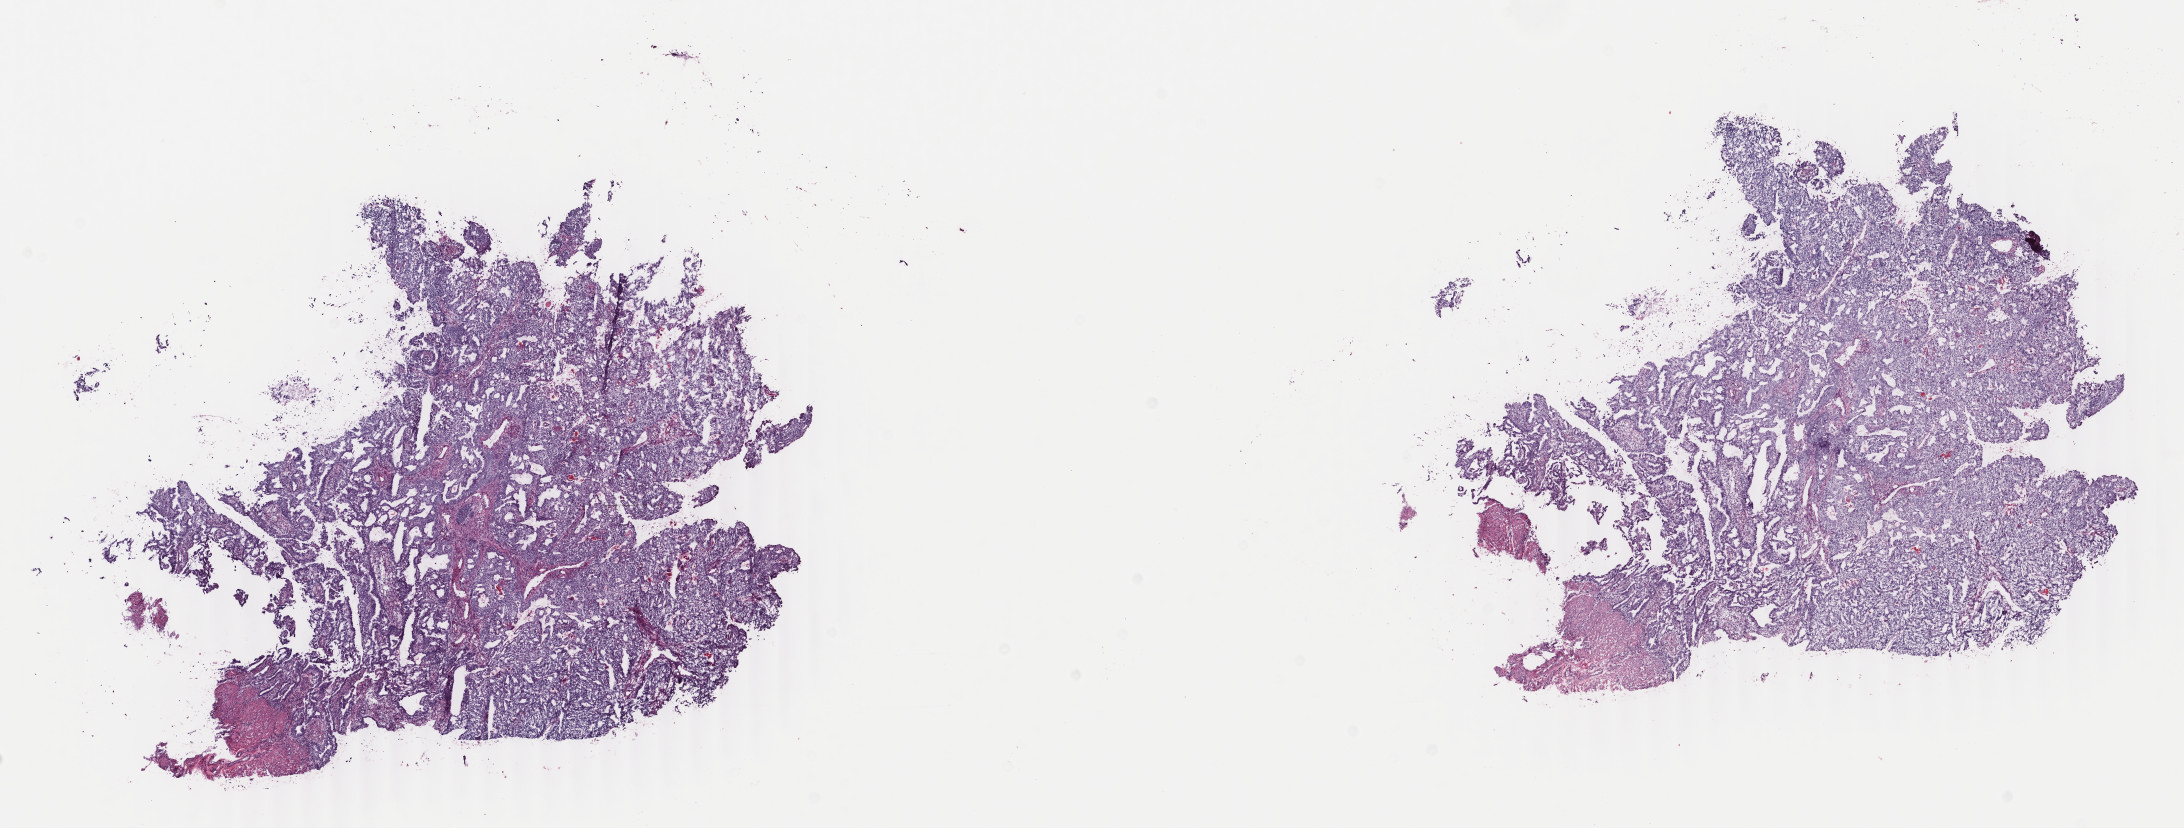
Digitized Hematoxylin and eosin (H&E) stained tissue section (whole slide), whole scanned area (about 17.4 x 6.6 mm, slide scanned at 40x) shown as a low-resolution overview; frozen section from the top of the tissue portion; uterus, primary tumour sample. Patient: female, age at initial diagnosis 34 years. Slide review estimates, as recorded: tumour cells 70%, tumour nuclei 80%.
Diagnosis: Endometrioid adenocarcinoma, secretory variant.